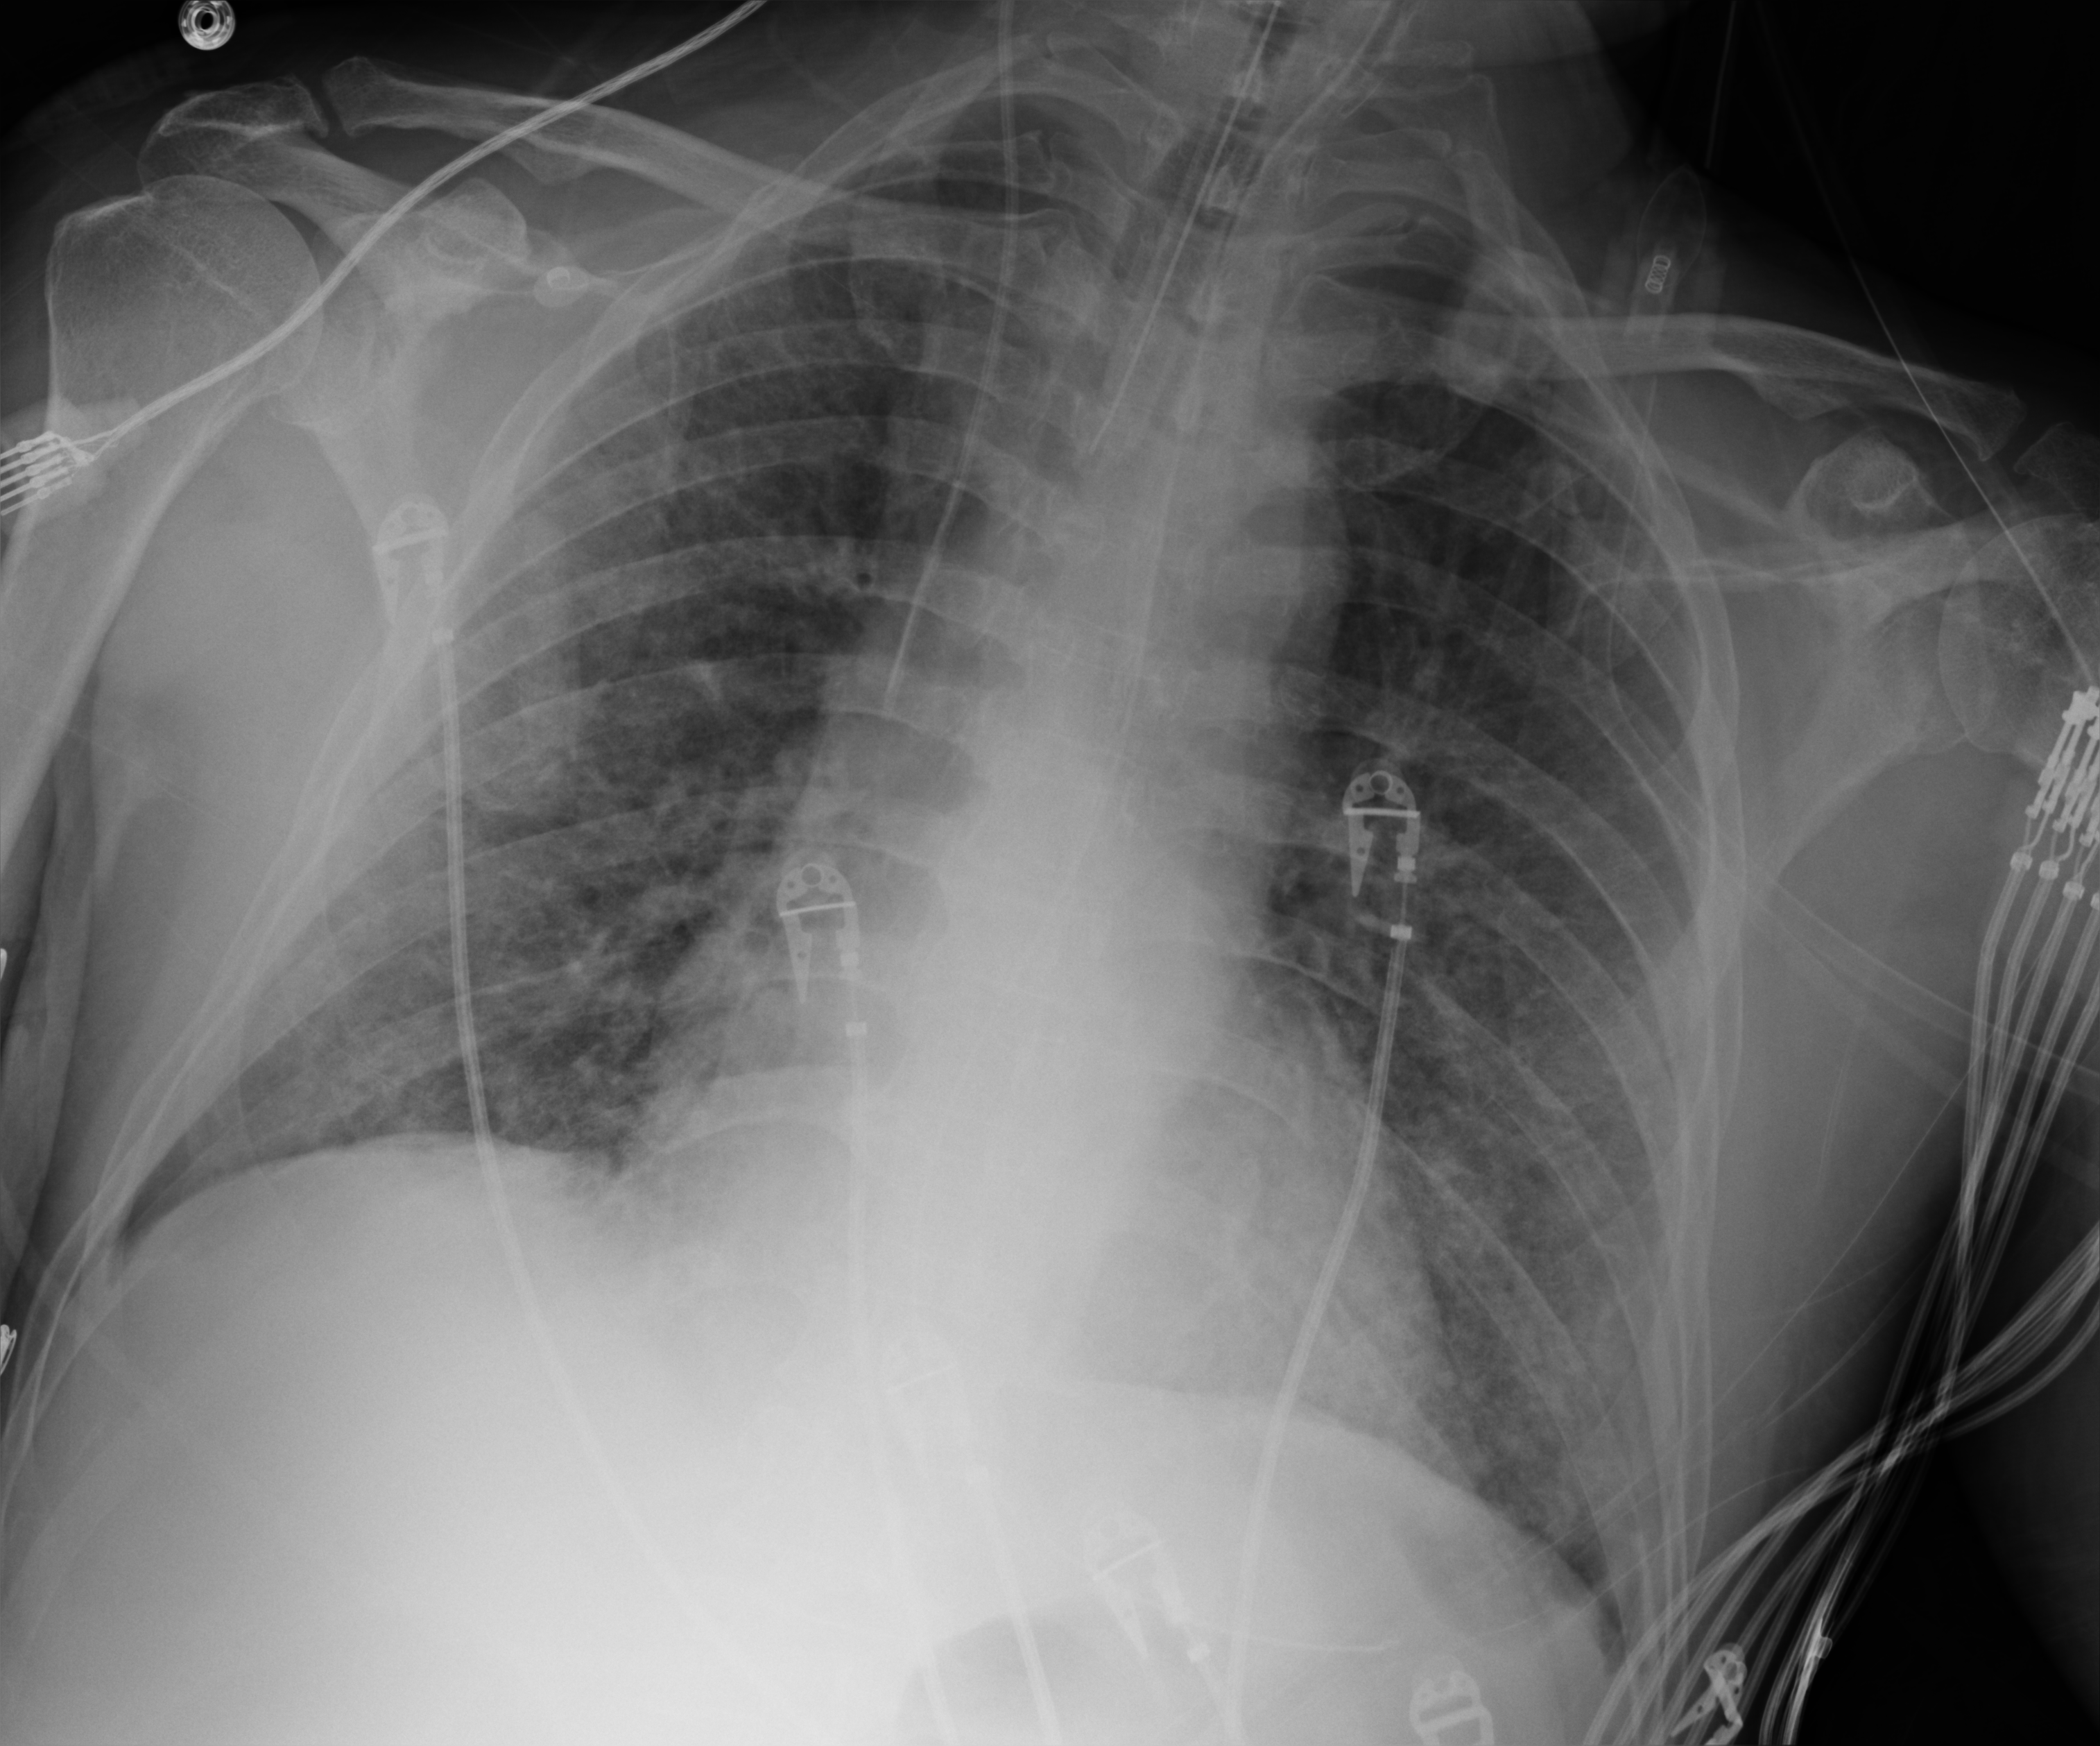
Bedside chest radiograph (computed radiography), anteroposterior (AP) projection. Male patient hospitalised with COVID-19, age 60–74 years.
Hospital-stay facts (about this admission, not read from this image; timing relative to this image not recorded): mechanically ventilated during this hospital stay: yes.